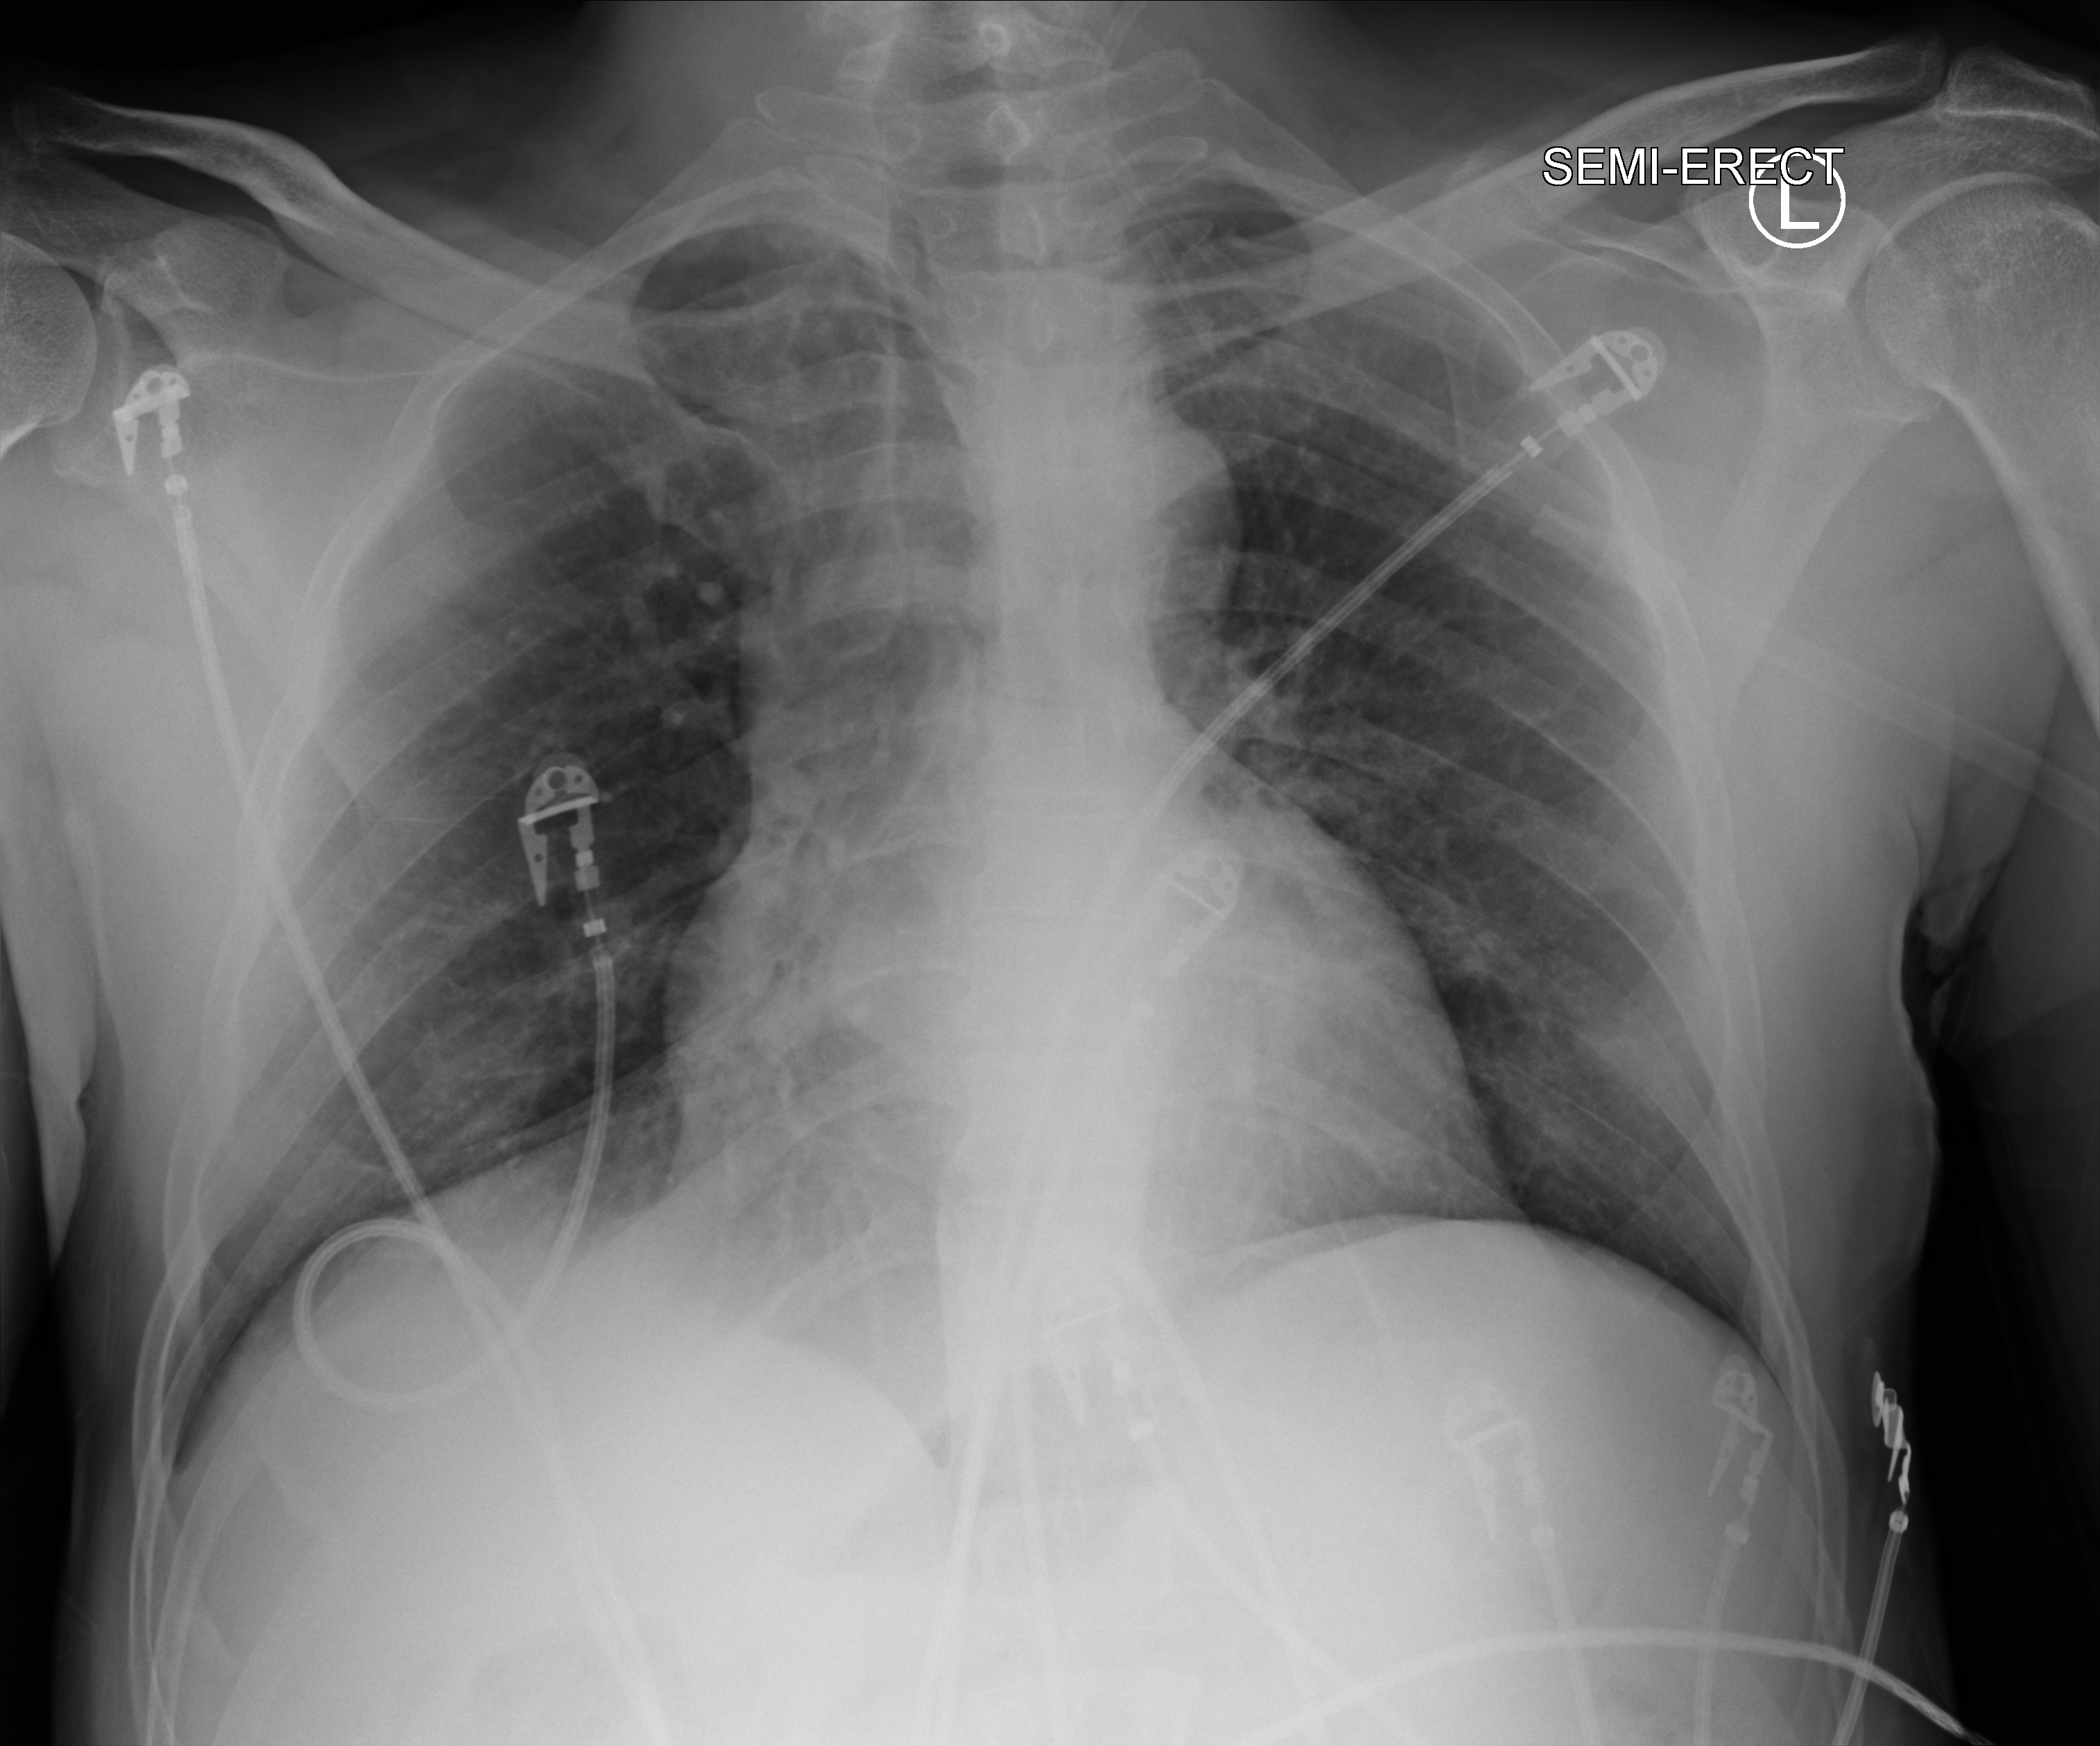
Chest X-ray (portable); anteroposterior (AP) projection. Patient hospitalised with COVID-19; male, aged 18–59 years.
From the hospital-stay record, not from the radiograph (when in the stay this image was taken is not recorded):
- diabetes (admission record): yes
- mechanically ventilated during this hospital stay: yes
- admitted to intensive care during this hospital stay: yes